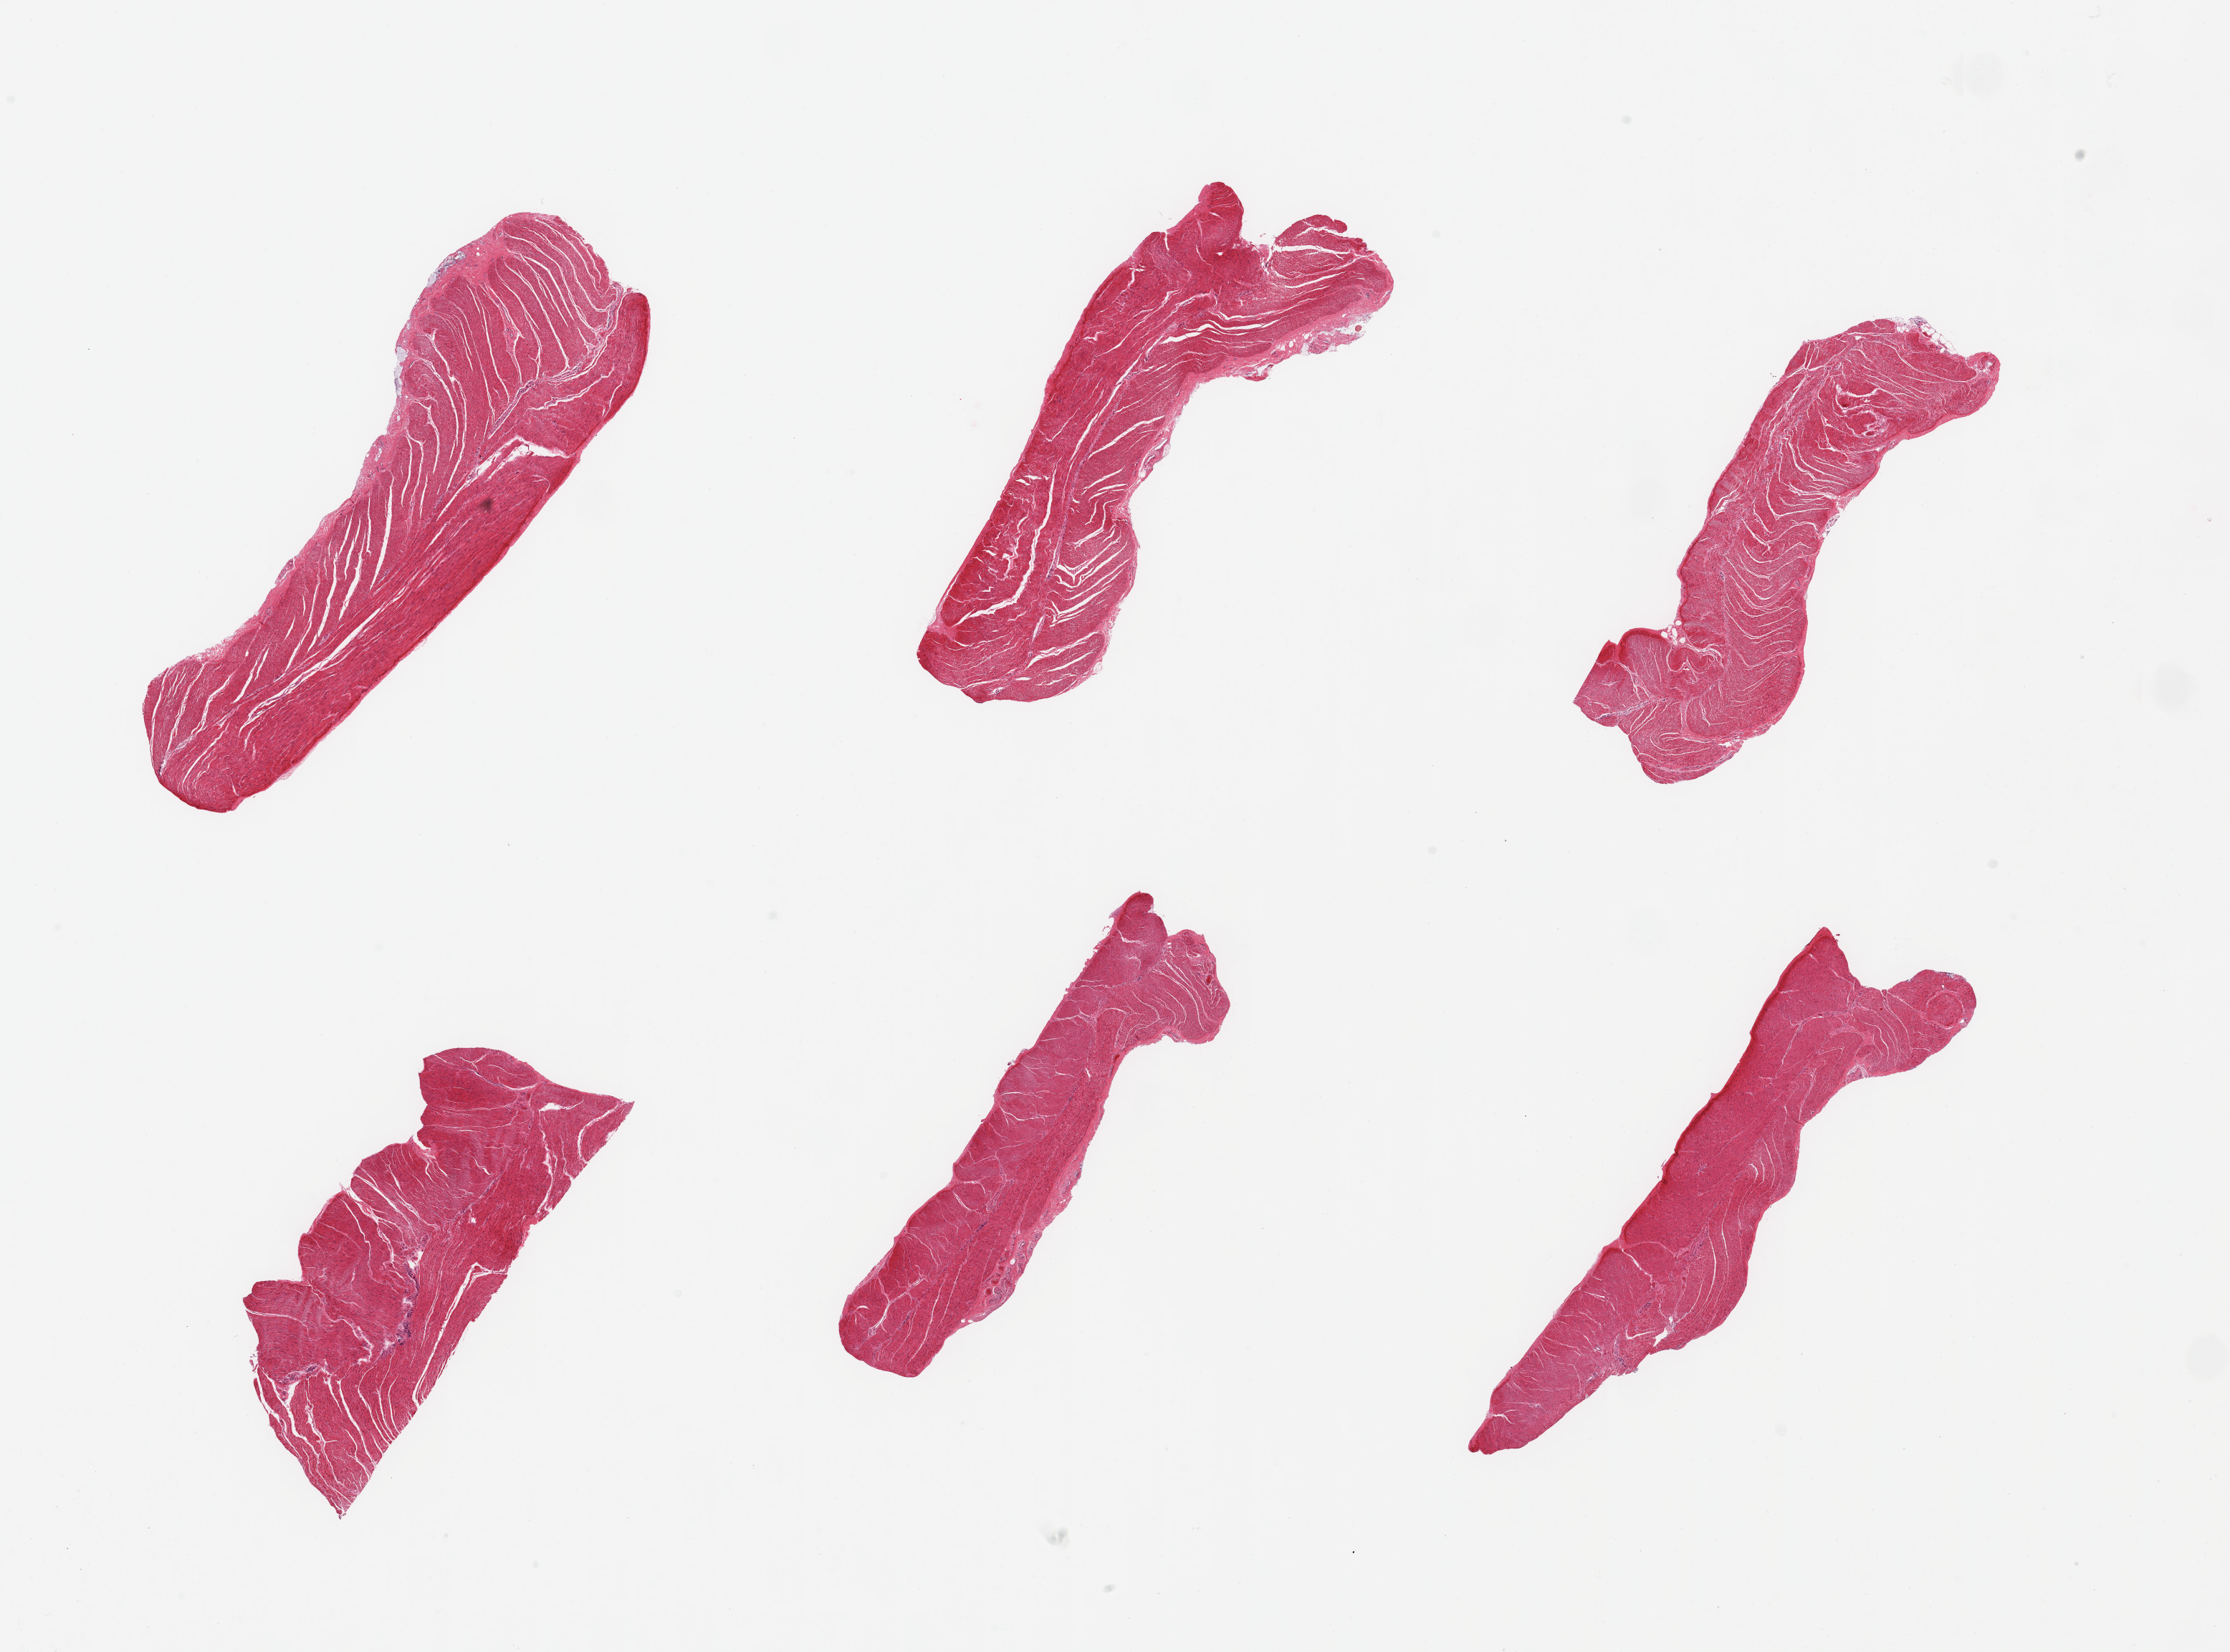
H&E whole-slide image, a low-resolution overview of the entire scanned area, about 24.6 x 18.2 mm (acquisition: 20x scan). PAXgene-fixed paraffin-embedded (PFPE) section. Section of sigmoid colon (target tissue). Tissue donor sample. Donor: male.
Review note (as recorded): 6 pieces, confirmed target muscularis.